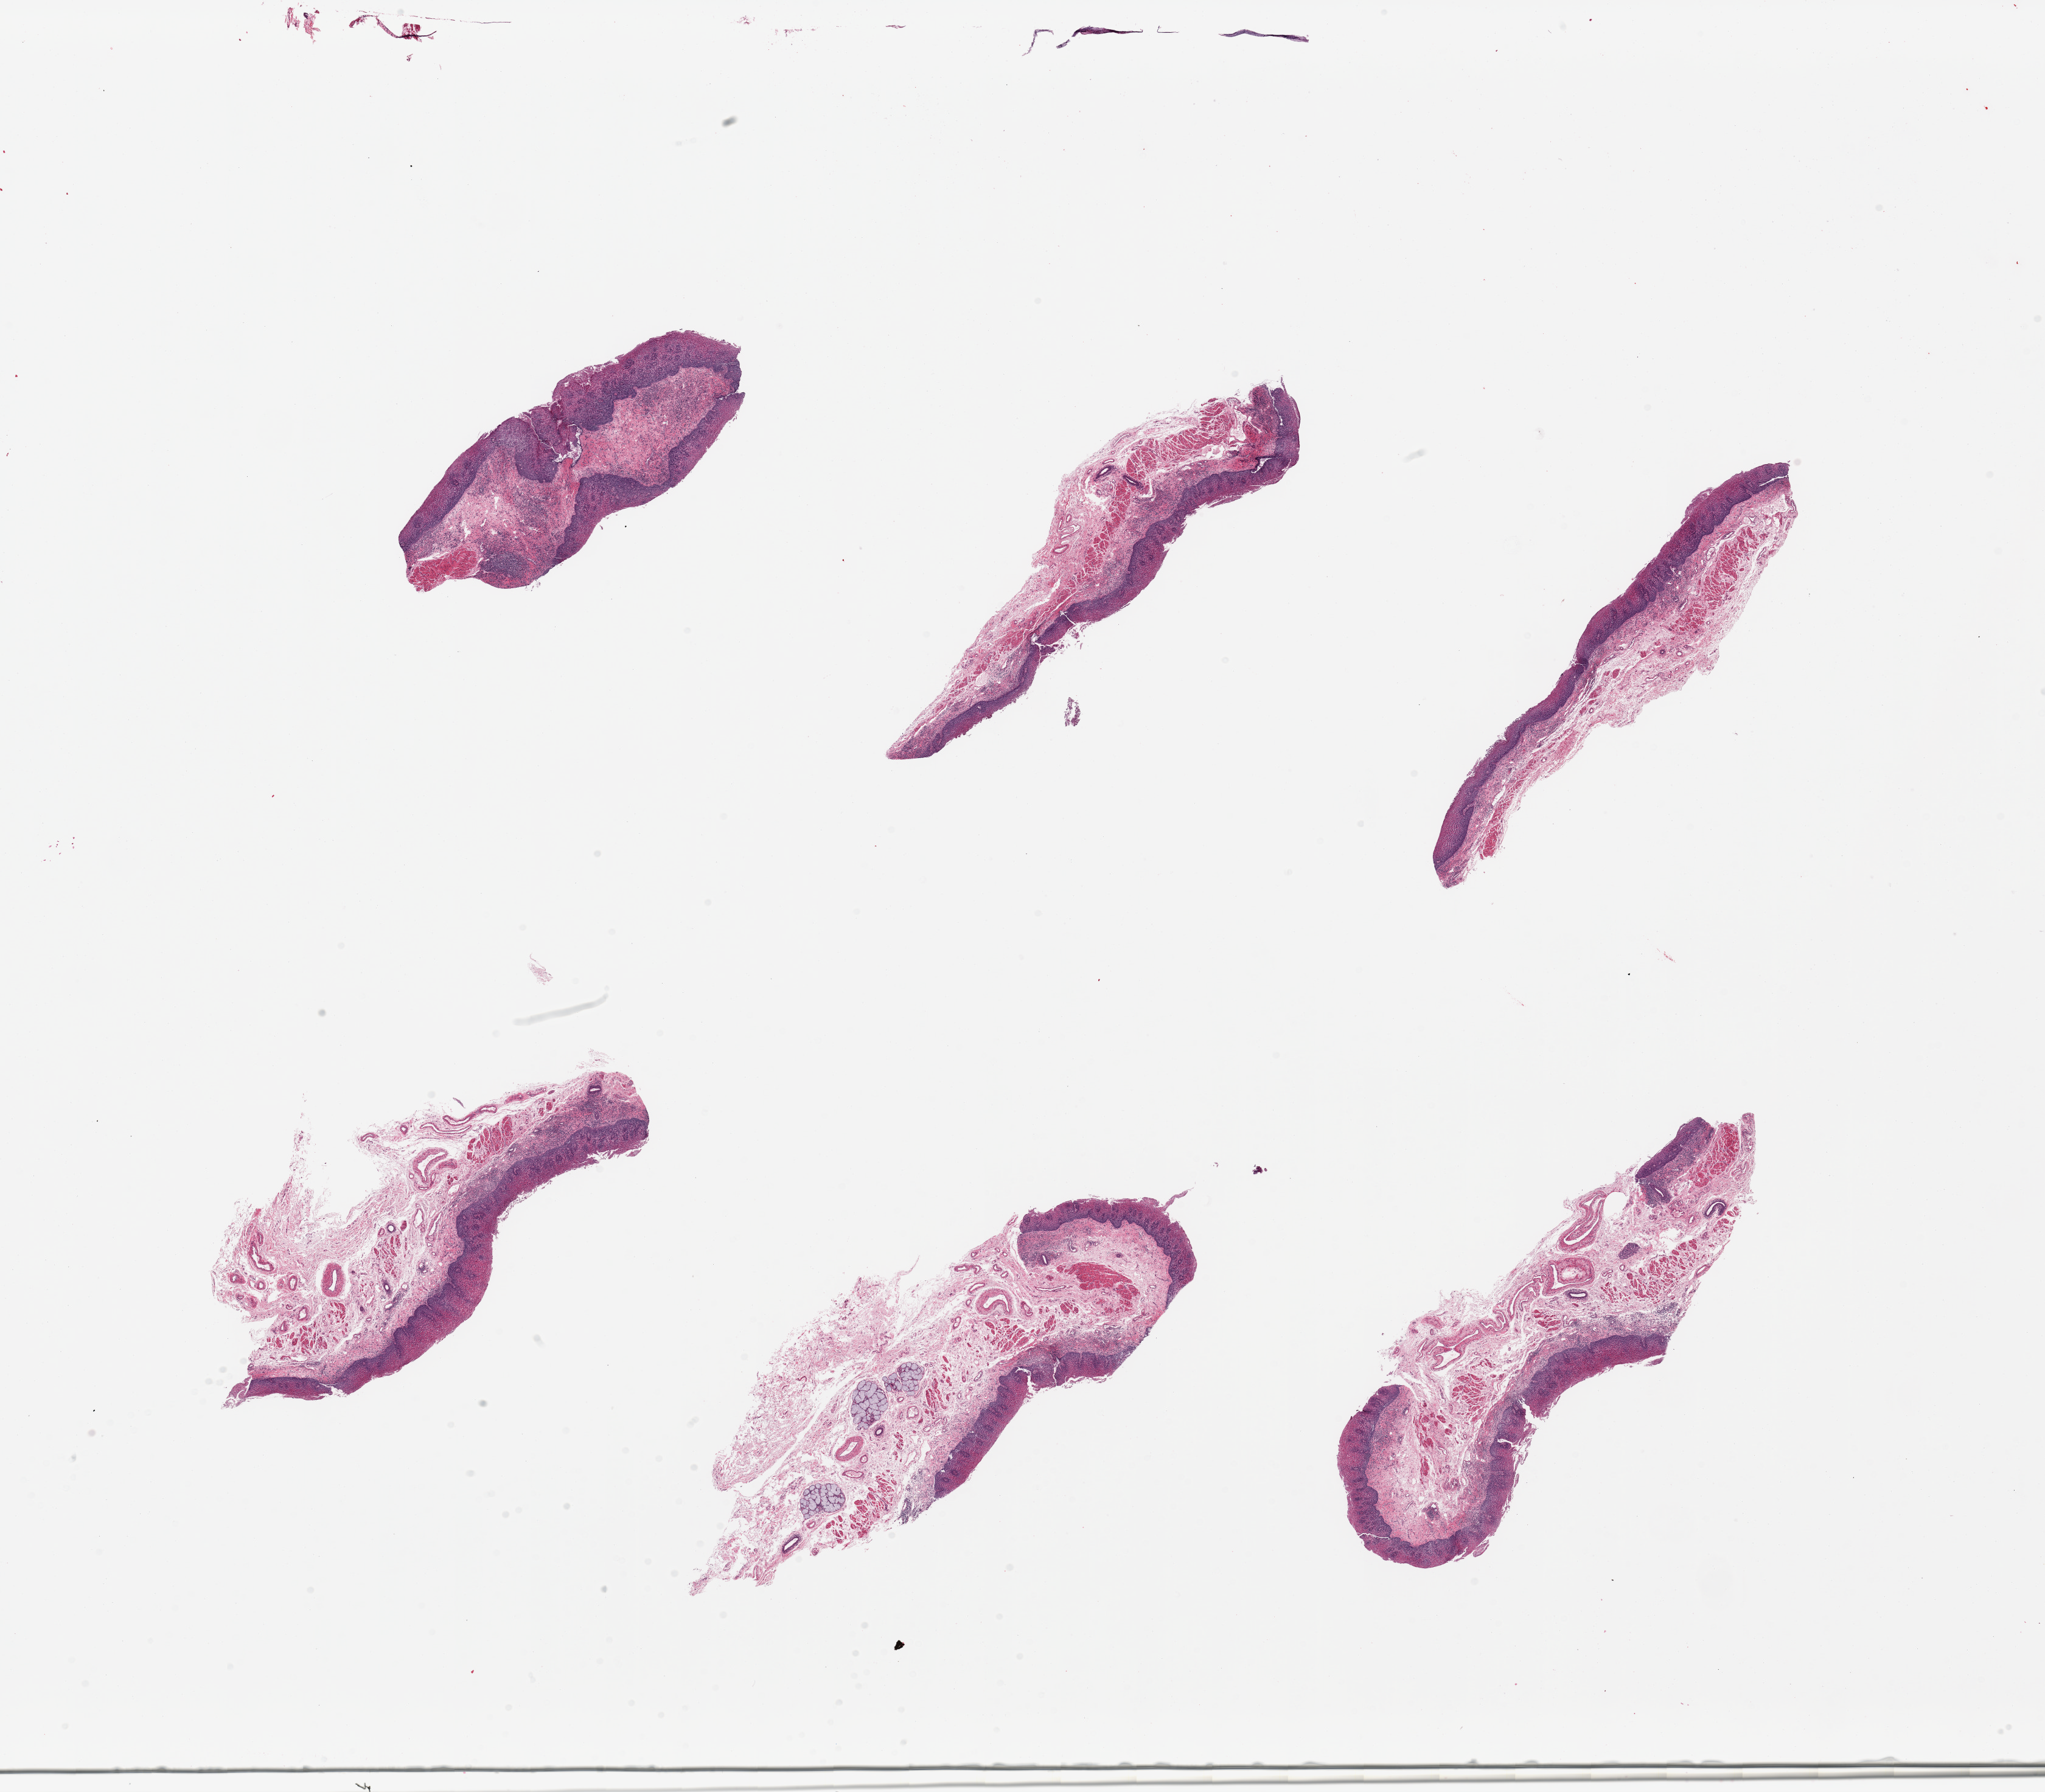
Digitized hematoxylin and eosin (H&E)-stained section, low-resolution overview of the scanned area, about 26.6 x 23.3 mm, PAXgene-fixed paraffin-embedded (PFPE) section, sampled site (target tissue): esophageal mucous membrane, tissue donor sample. Donor: female.
Reviewer comment on this tissue sample: 6 pieces, aquamous mucosa up to ~0.3 mm, 30% thickness.